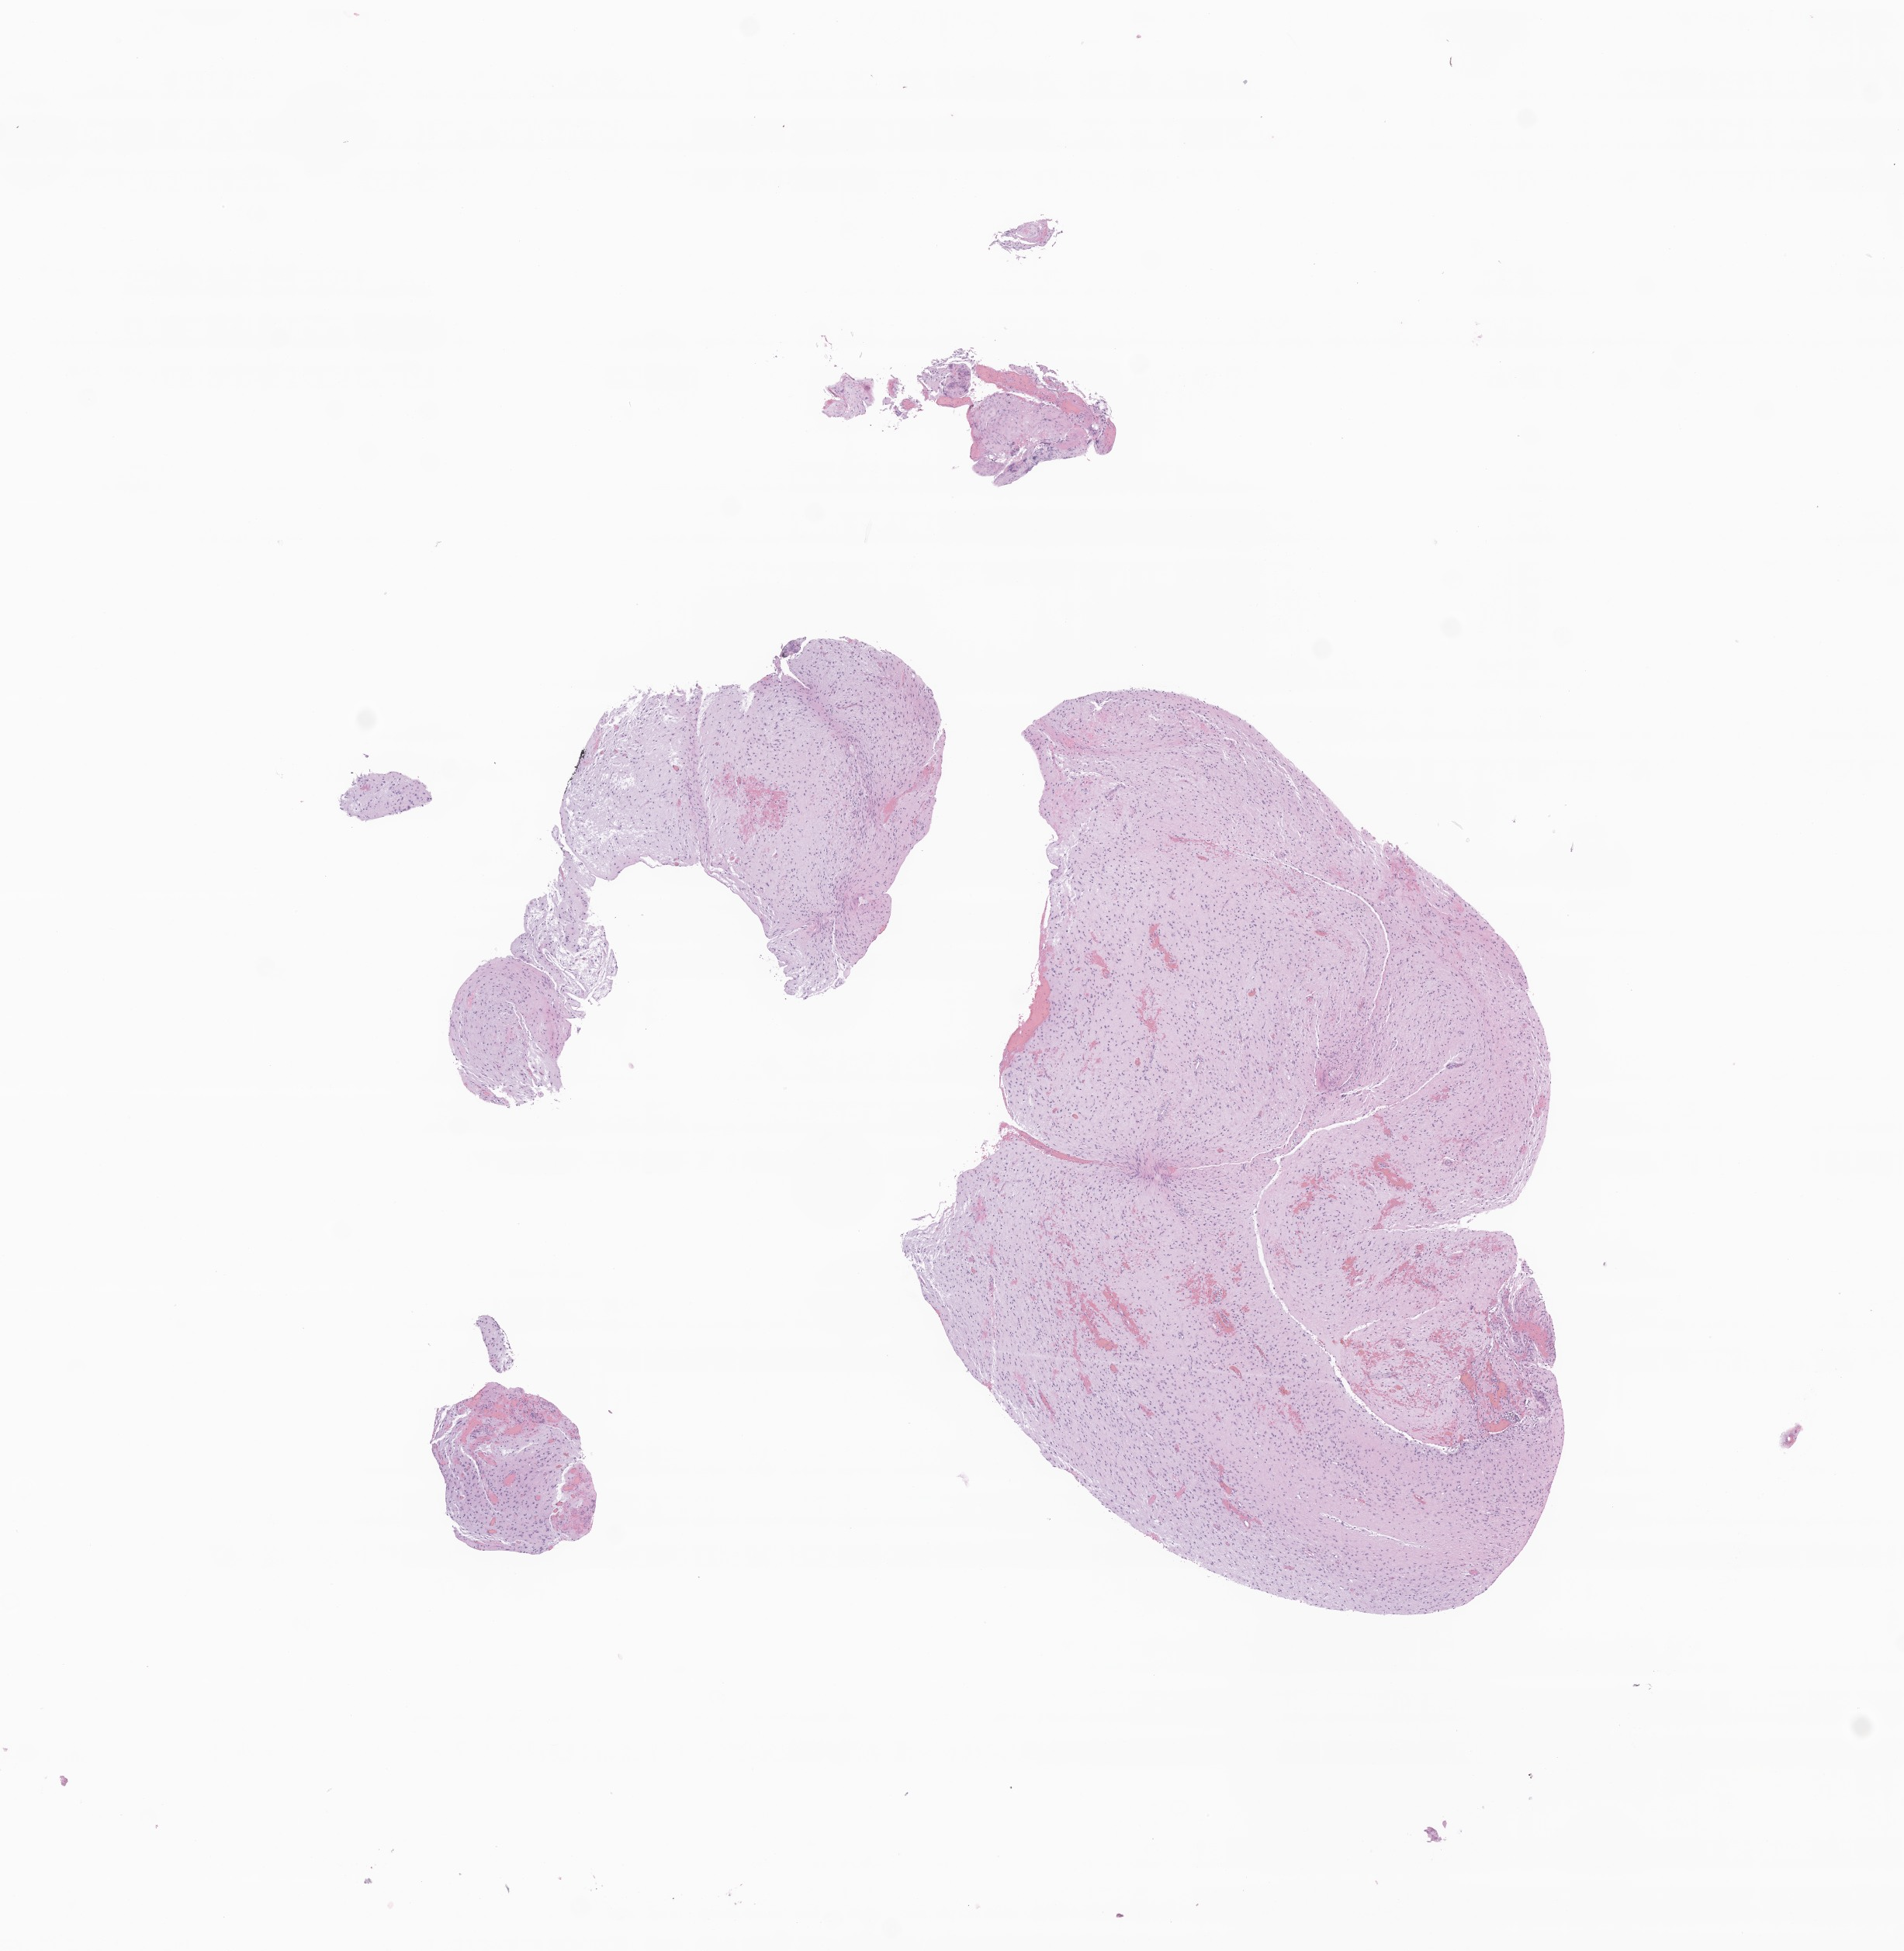
Whole-slide image, haematoxylin and eosin stain of tumor tissue from the brain, low-resolution overview of the scanned area, about 10.3 x 10.6 mm; formalin-fixed paraffin-embedded section. Patient: male, age 225 months (18 years 9 months).
- recorded diagnosis: Pilocytic astrocytoma